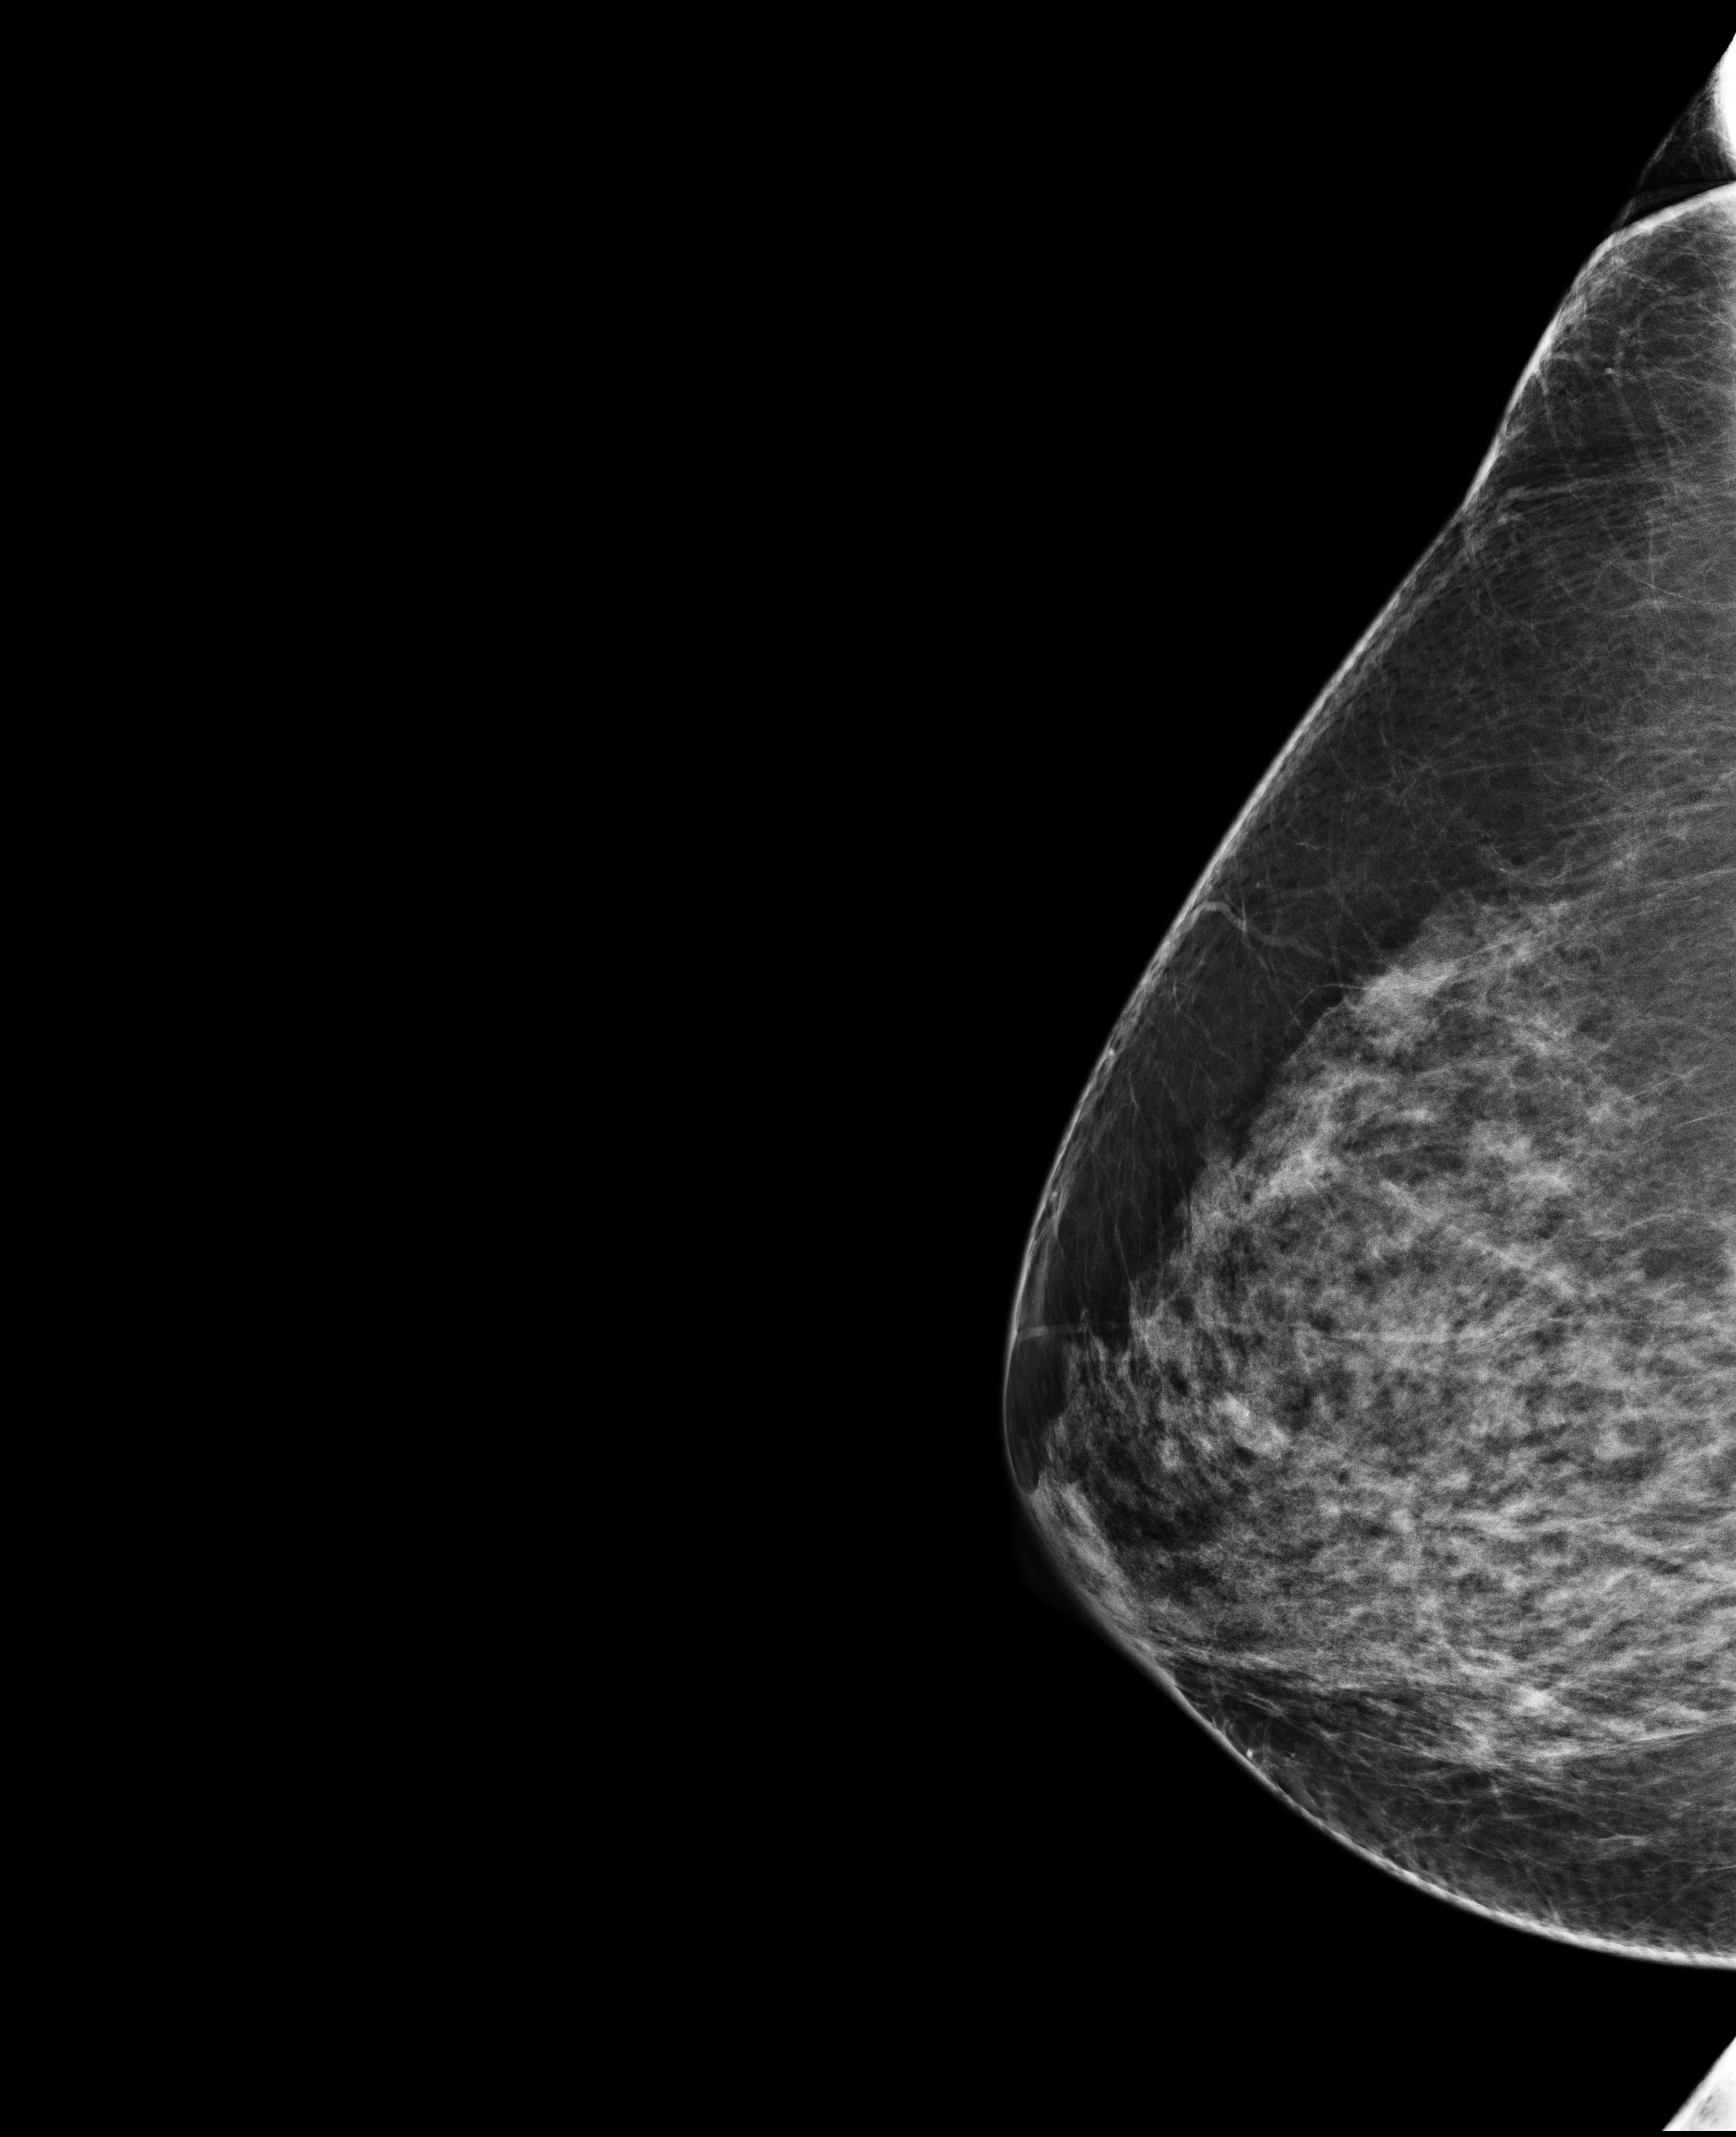
Annual screening mammography examination; compressed breast thickness 80 mm. Female patient, age 53 years.
Image type: full-field digital mammogram. Breast: right. Projection: exaggerated CC view (lateral).